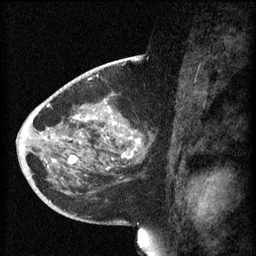
Breast MRI (dynamic contrast-enhanced), one sagittal slice; position 30 of 60 along the scan axis; 3 images stored at this slice position (order not interpretable as contrast timing); 1.5 T; TE 4.2 ms, TR 8.1 ms; 2 mm slice thickness; 256 × 256 image matrix, field of view 200 × 200 mm. Patient: female, 44 years.
Annotated regions visible in this slice (semi-automatically segmented with operator editing):
- analysis volume of interest (the breast-tissue region the enhancement analysis was run in; not a lesion): bounding box (x1, y1, x2, y2) in pixels: (59, 110, 151, 169)
- tumour enhancement mask (voxels above the 70 % enhancement threshold inside the analysis volume of interest): (67, 110, 140, 169)